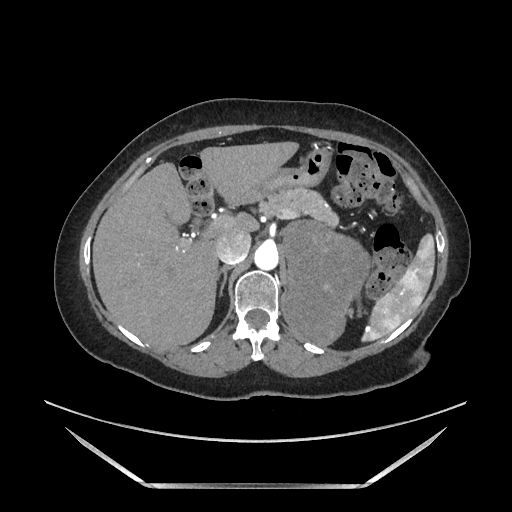
Contrast-enhanced abdominal CT, one axial slice; position 119 of 205 along the scan axis; soft-tissue window (W 400 / L 40 HU); 1.25 mm slice thickness; 512 × 512 image matrix, field of view 440 × 440 mm. Female patient. From the clinical record (not read from this slice): diagnosis: adrenocortical carcinoma; tumour side: left adrenal; tumour size at pathology: 12.5 cm; Ki-67 index: 39 %.
Outlined on this slice (semi-automatically segmented with operator editing):
- mass: bounding box [x1, y1, x2, y2] px = [288, 222, 370, 345]